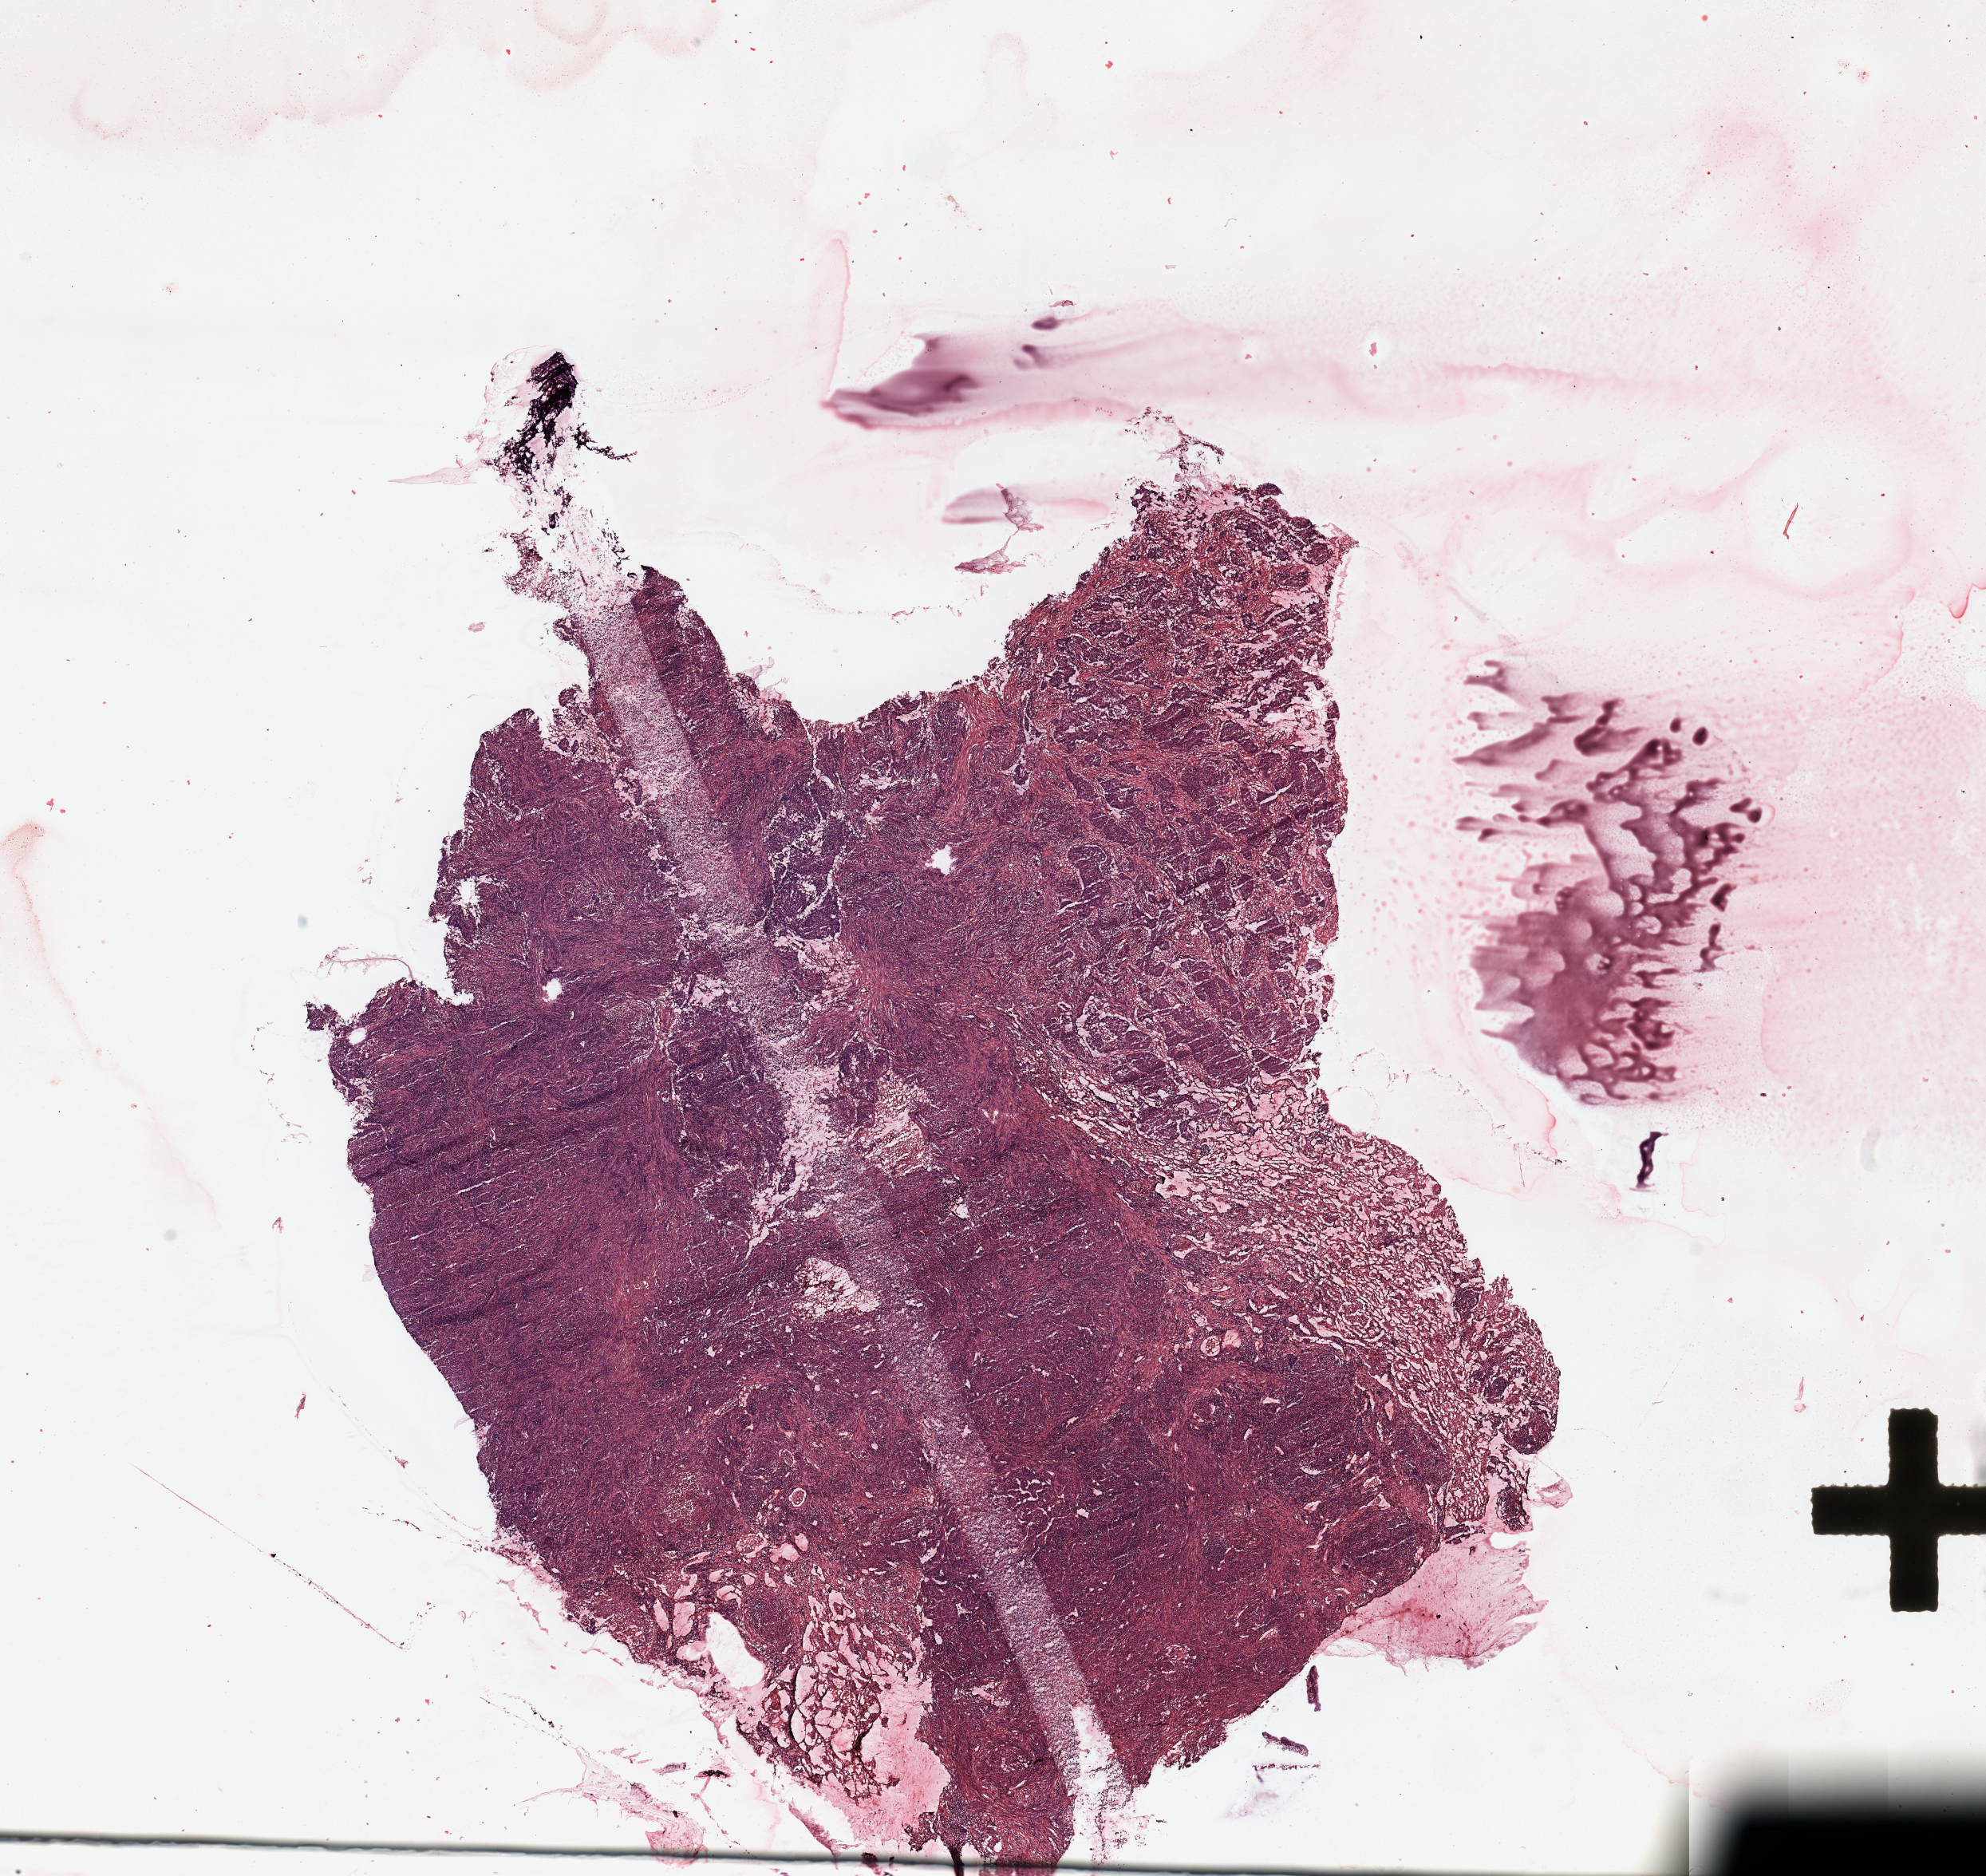
Hematoxylin and eosin (H&E) stained whole-slide image — whole scanned area (about 19.7 x 18.6 mm, acquisition: 20x scan) shown as a low-resolution overview. Tumour tissue sample, lung. Patient: male, age 67 years.
Primary tumour site (as recorded): left upper lobe. Patient diagnosis (cohort enrolment): squamous cell carcinoma (lung).